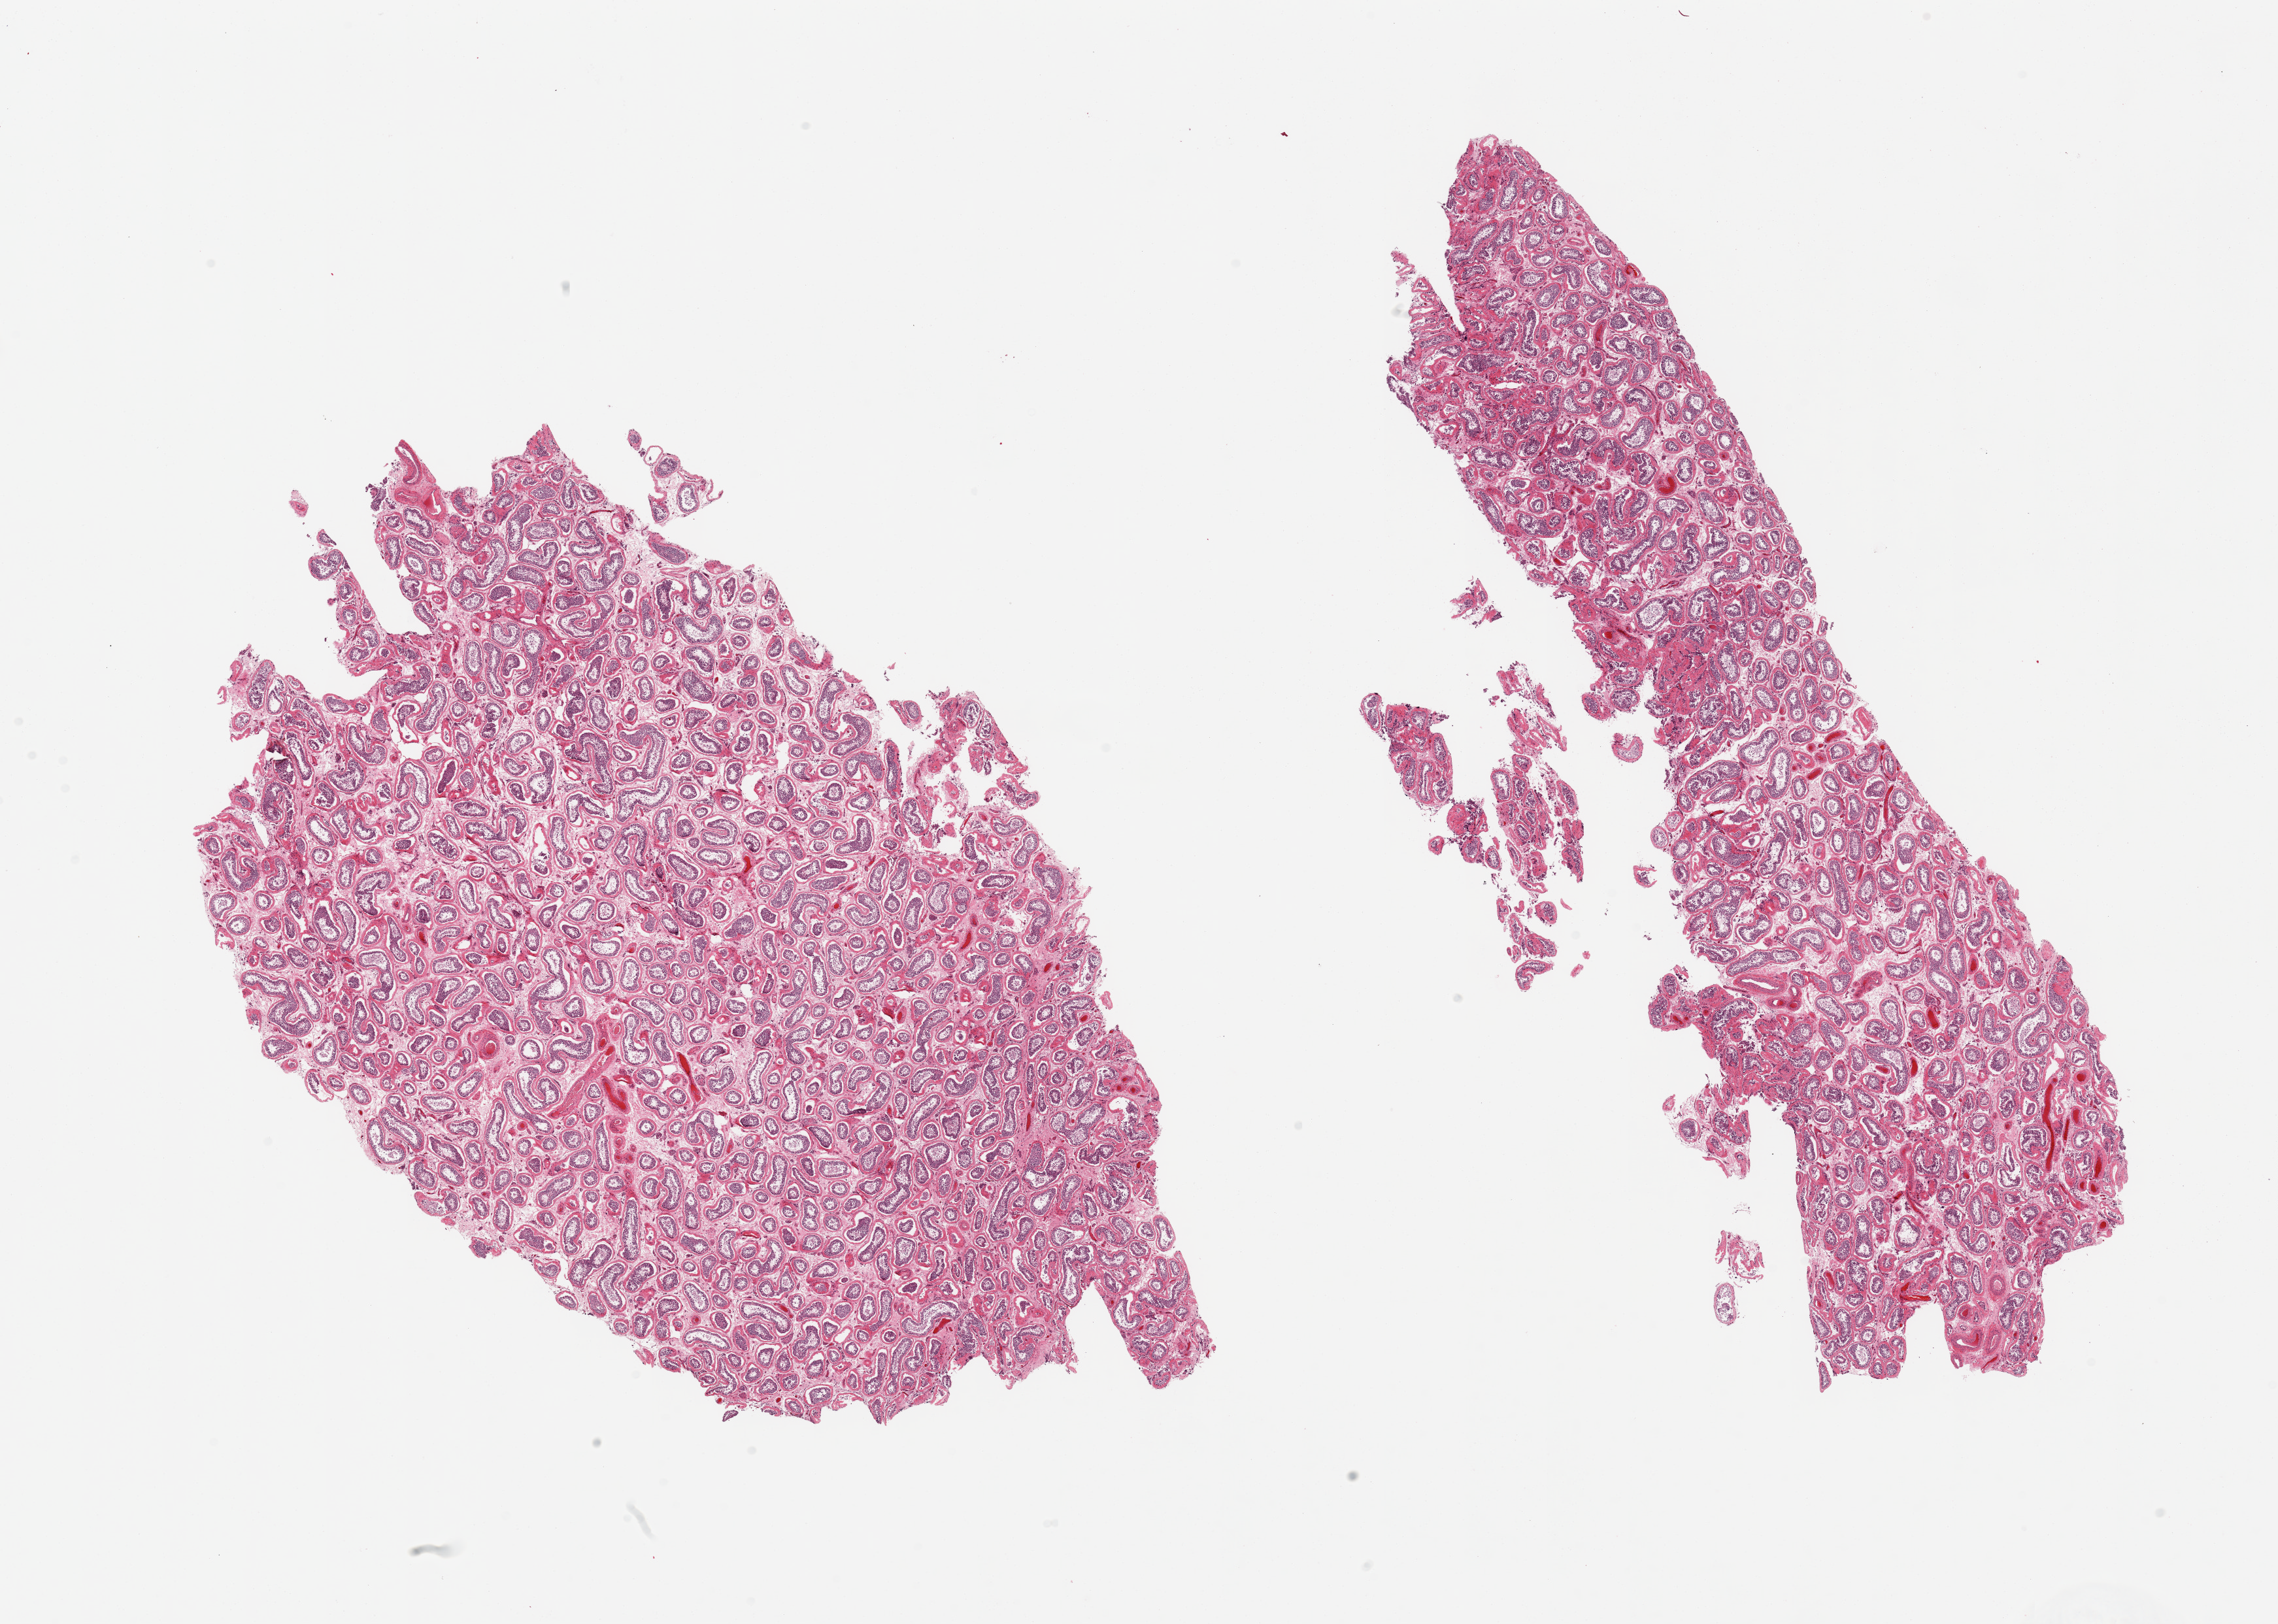
Digitized haematoxylin and eosin-stained section — whole scanned area (about 27.6 x 19.7 mm, acquisition: 20x scan) shown as a low-resolution overview. PAXgene-fixed paraffin-embedded (PFPE) section. Target tissue: testis. Donor tissue sample.
* pathologist's review note for this sample: 2 pieces; increased peritubular fibrosis, spermatogenesis is present